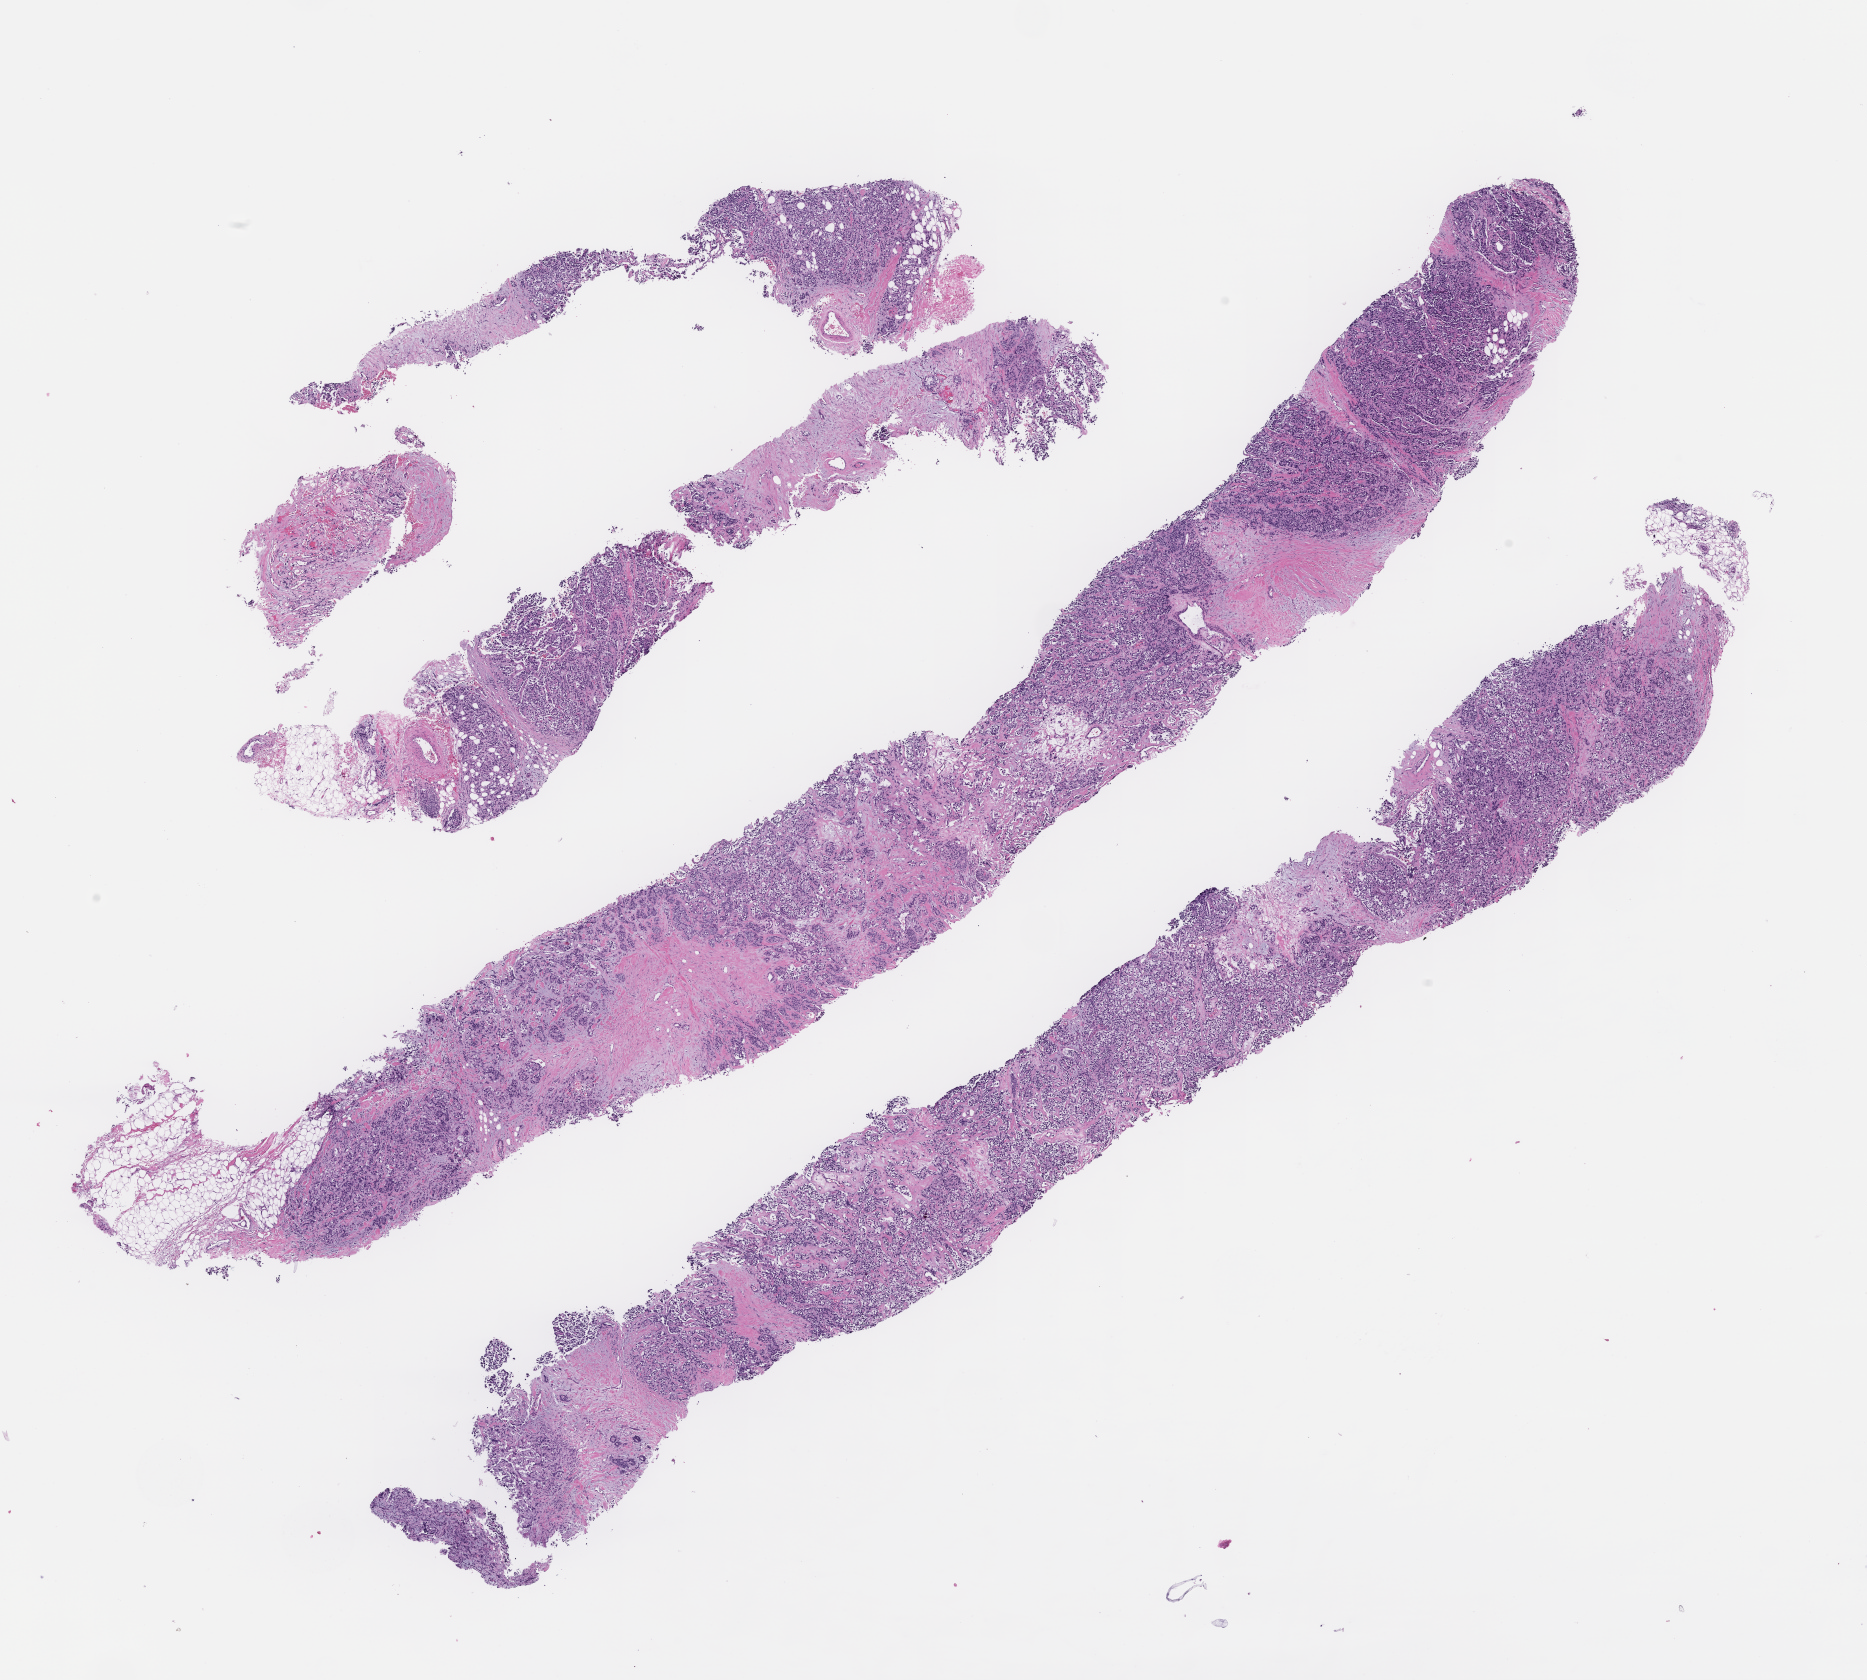
Whole-slide image, haematoxylin and eosin stain, a low-resolution overview of the entire scanned area, about 15.1 x 13.6 mm; formalin-fixed paraffin-embedded section; site: breast; archival tissue. Patient: female.
* this section: primary tumor
* diagnosis: Invasive Breast Carcinoma